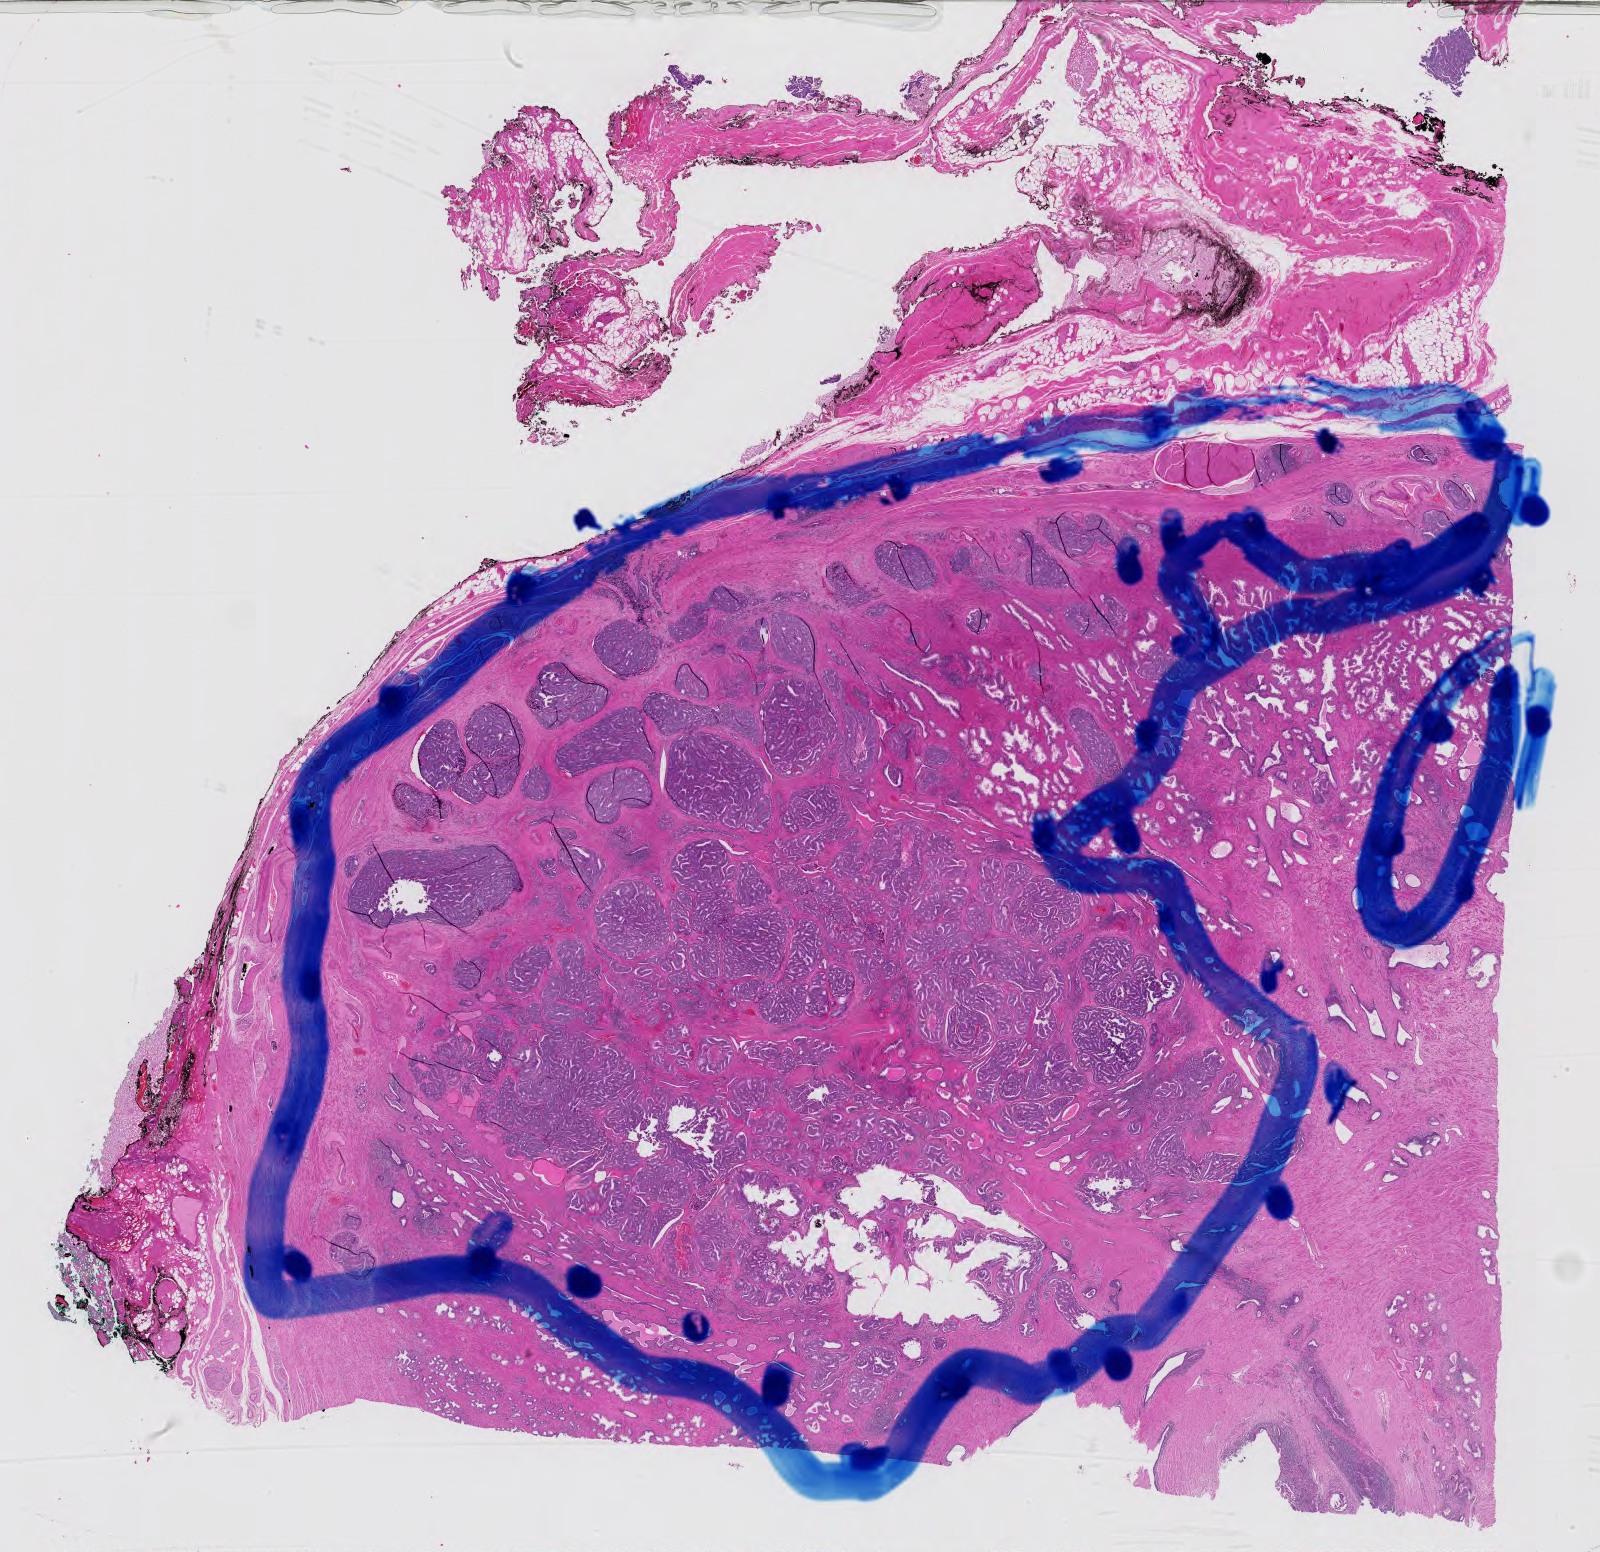
H&E whole-slide image, shown as a low-resolution overview of the whole scanned area (about 23.2 x 22.5 mm, slide scanned at 40x), FFPE section, prostate, primary tumour sample. Patient: male, age at initial diagnosis 74 years. Gleason score: 8 (4+4).
• laterality: bilateral
• diagnosis: Adenocarcinoma, NOS